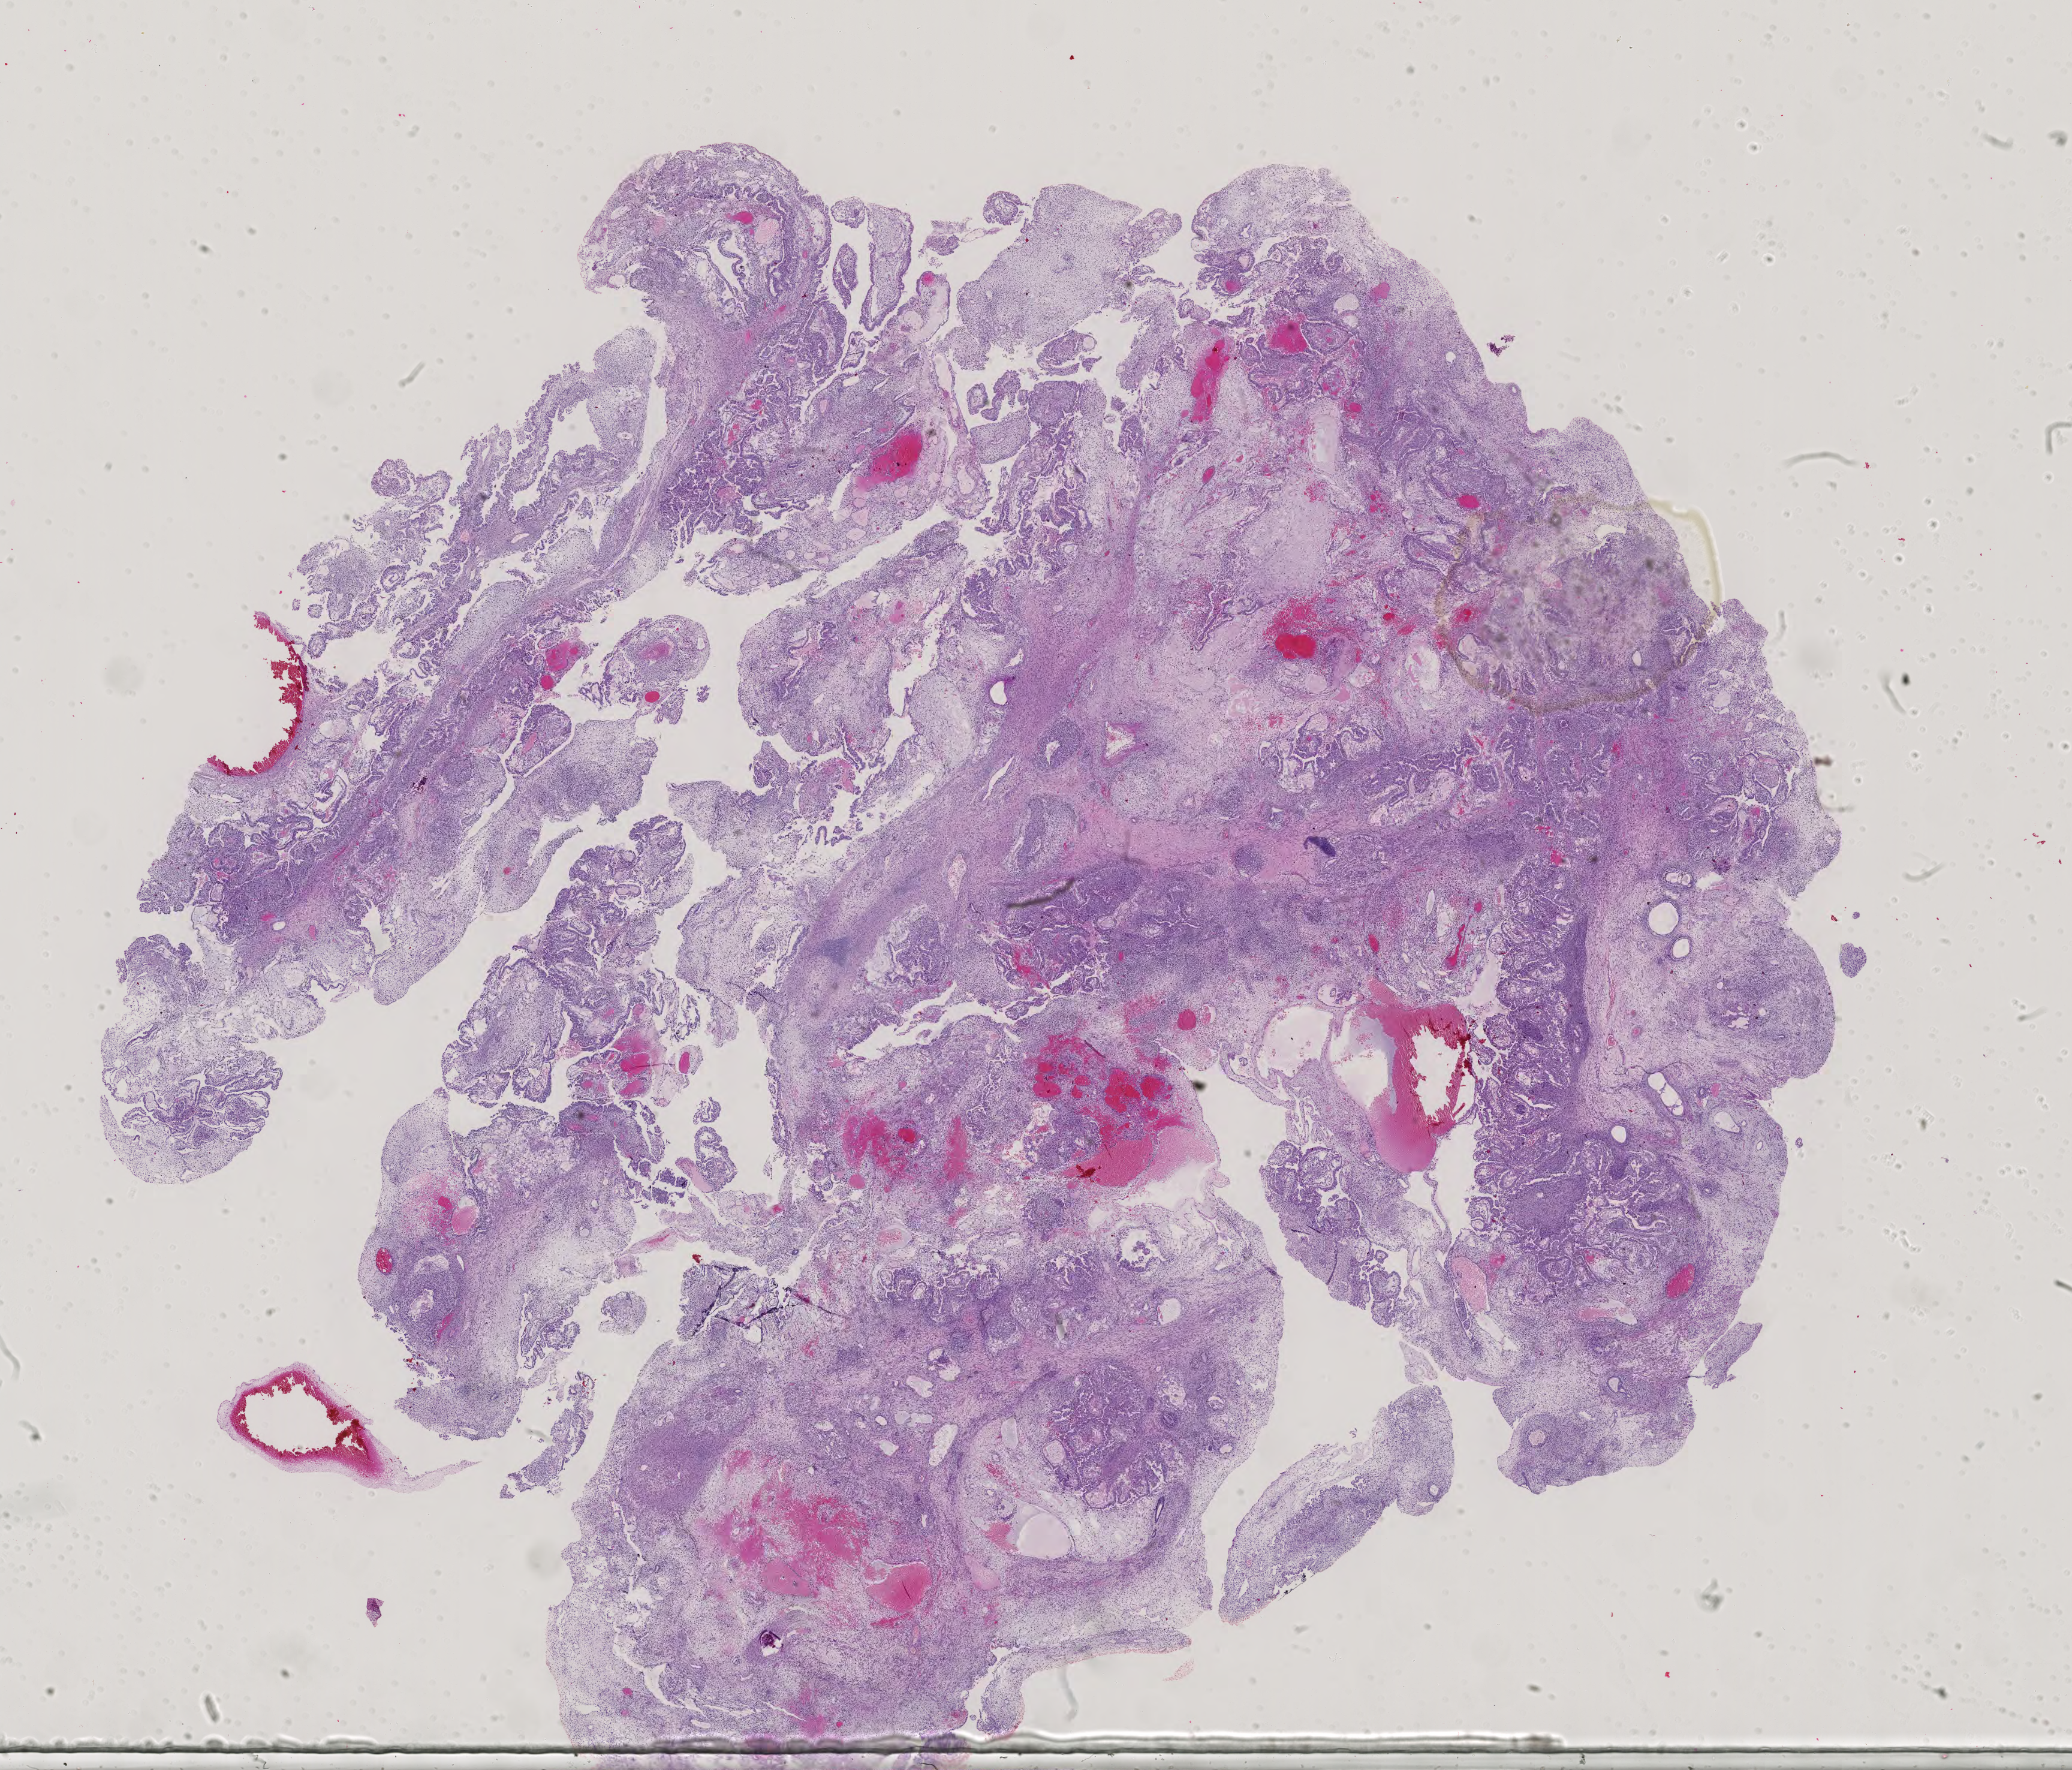
Hematoxylin and eosin (H&E) stained whole-slide image, a low-resolution overview of the entire scanned area, about 25.2 x 21.5 mm; formalin-fixed paraffin-embedded (FFPE) diagnostic section; primary tumour sample from the testis. Male patient; age at initial diagnosis 39 years.
AJCC pathologic stage: IIIB. Histologic diagnosis: Mixed germ cell tumor.